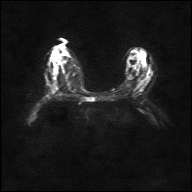
Breast MRI, one axial slice; position 15 of 36 along the scan axis; diffusion-weighted series; image 2 of 4 stored at this slice position (different b-values; order by instance number); 1.5 T; 4 mm slice thickness; 192 × 192 image matrix. Female patient.
Annotated regions visible in this slice (expert manual segmentation):
- tumour on diffusion-weighted imaging: box from (x=51, y=88) to (x=55, y=92) px